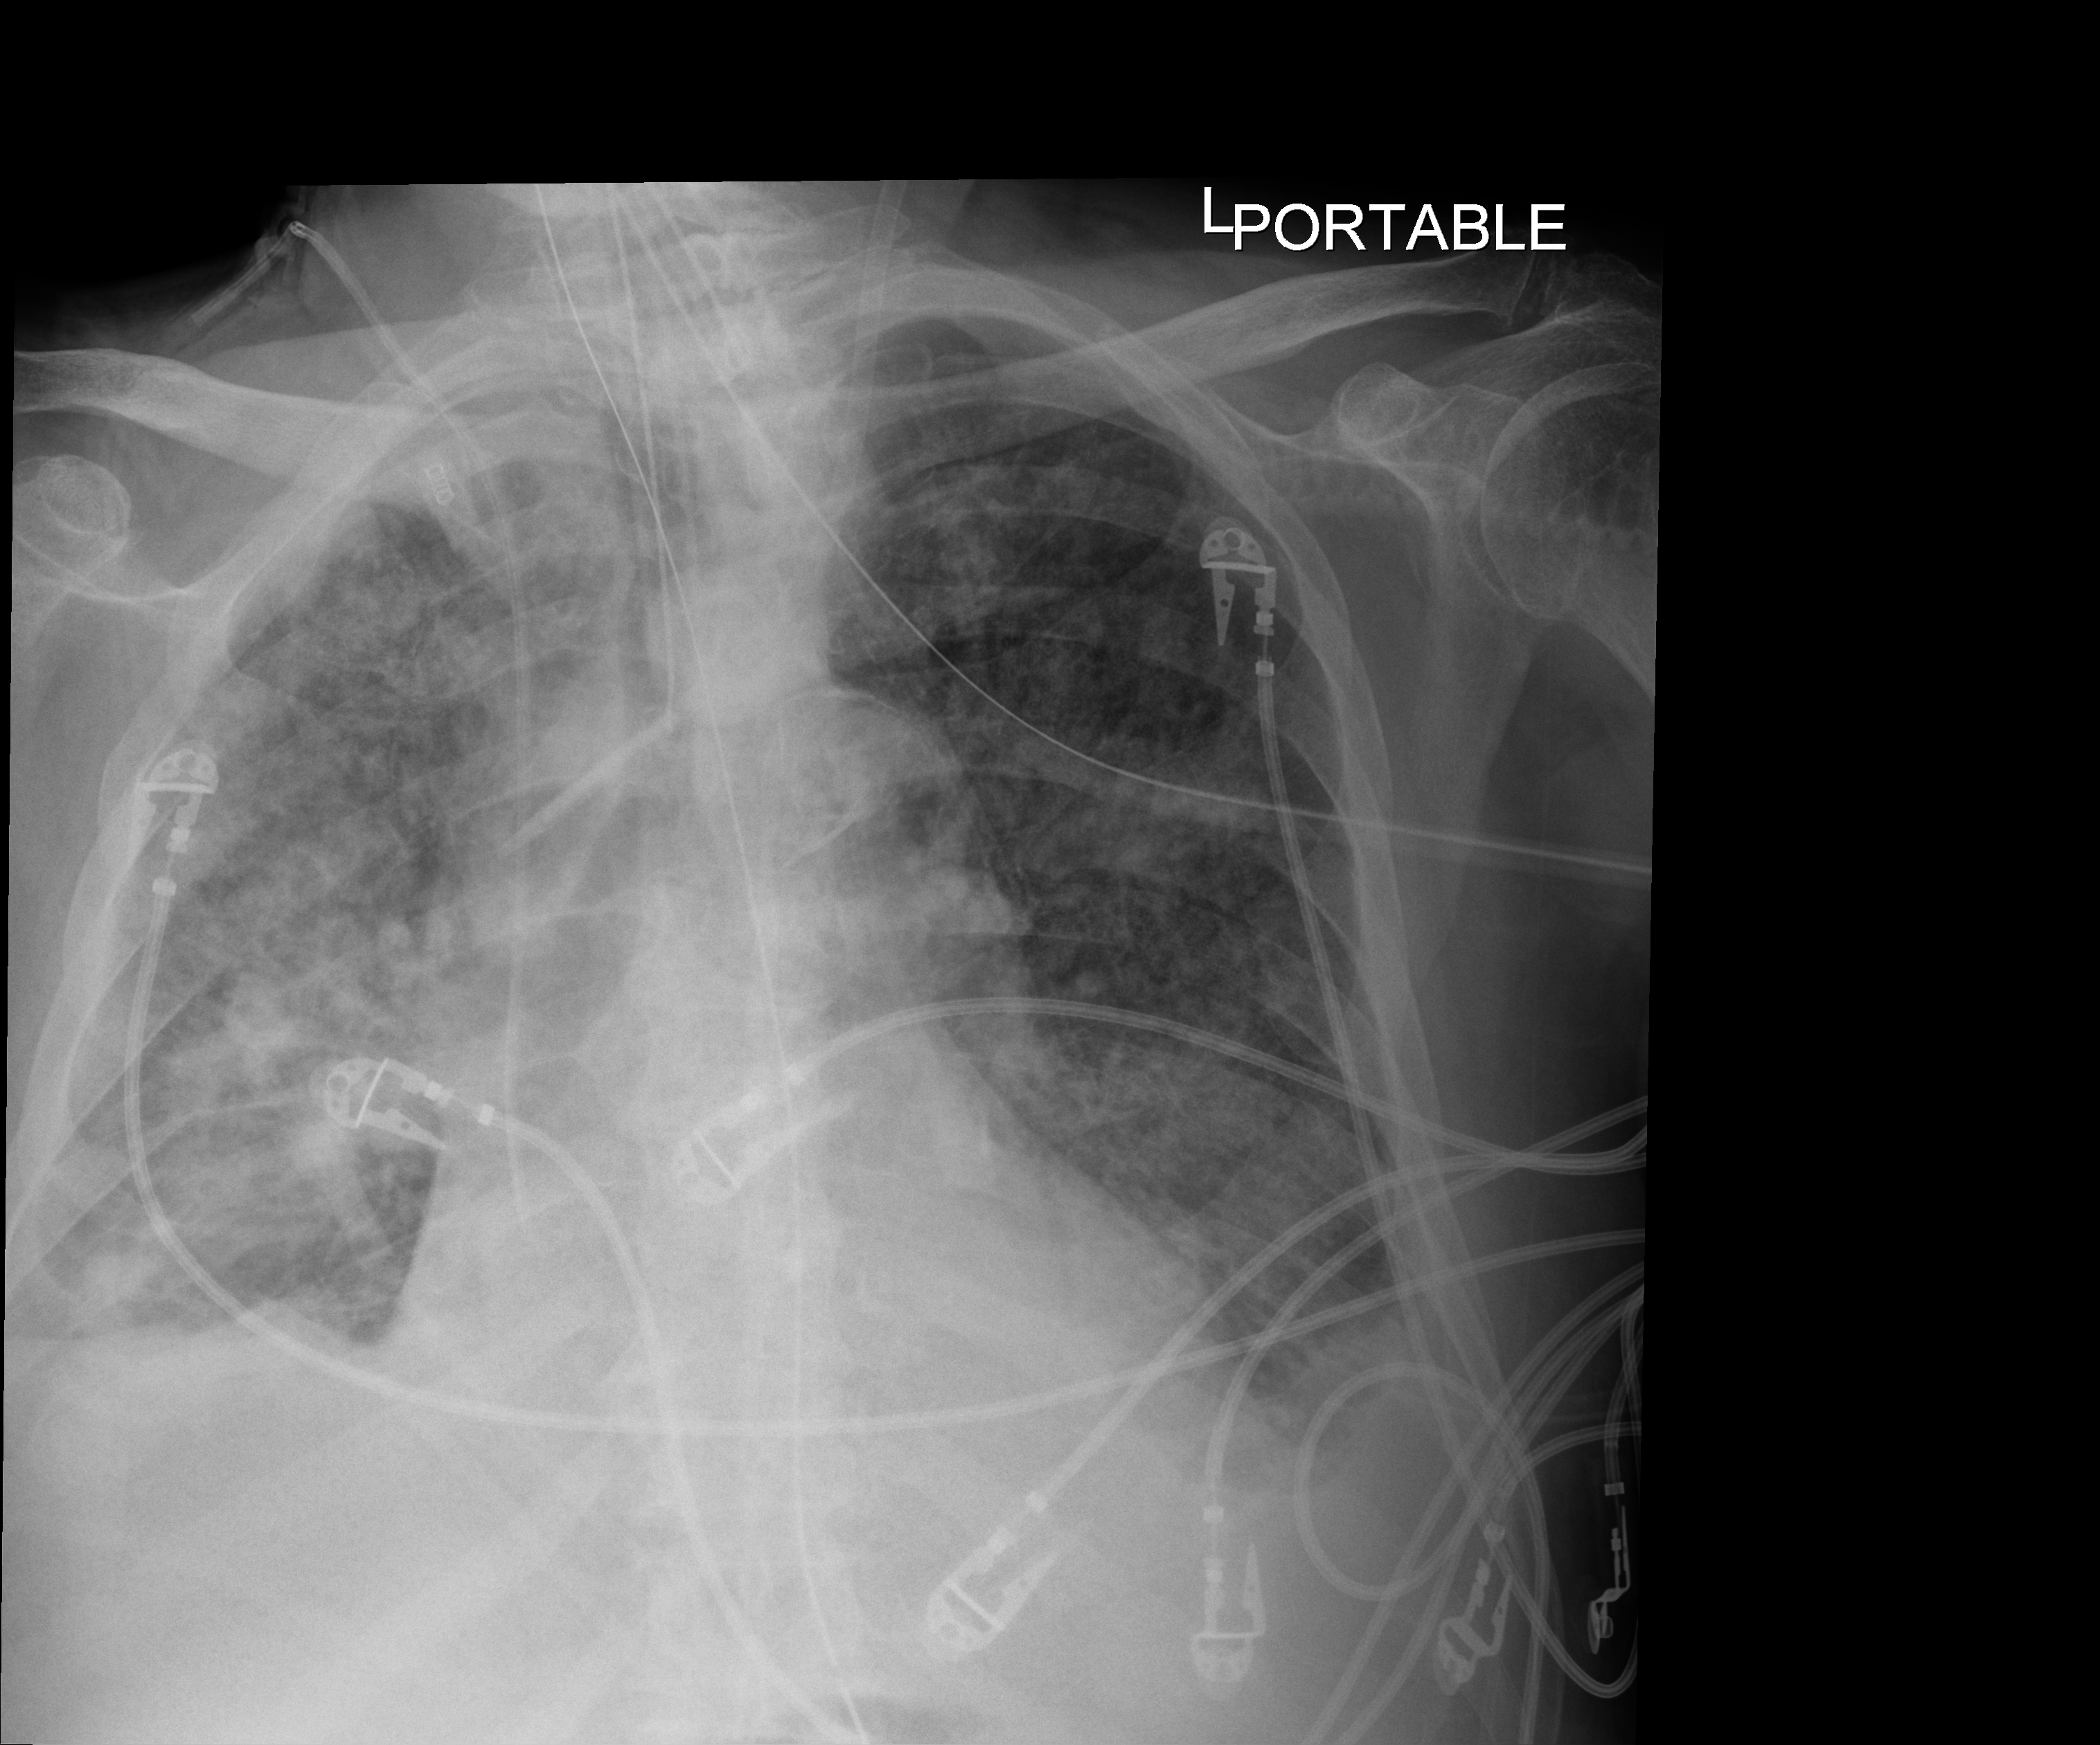
Portable chest radiograph, anteroposterior (AP) projection. Patient hospitalised with COVID-19; male, aged 75–90 years.
Hospital-stay facts (about this admission, not read from this image; timing relative to this image not recorded):
- mechanically ventilated during this hospital stay: yes